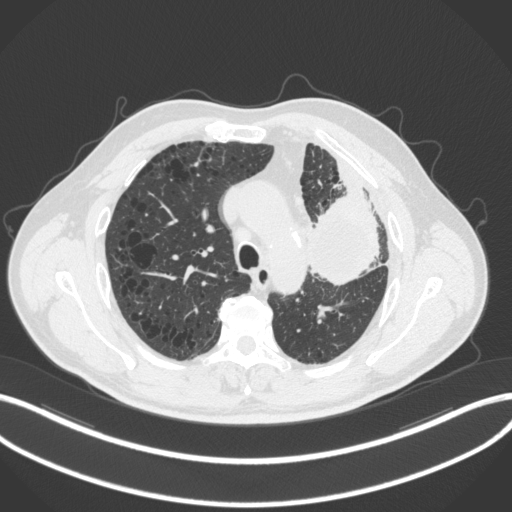
Chest CT, one axial slice; position 211 of 286 along the scan axis; lung window (W 1500 / L -600 HU); 512 × 512 image matrix, field of view 400 × 400 mm. Patient: male, 68 years. Case-level facts recorded for this patient, not image findings: clinical TNM (as recorded): T3 N3 M1.
Outlined on this slice (rectangle marked by the reading radiologist):
- lung tumour (recorded histology: adenocarcinoma): bounding box <306,188,383,289> (left, top, right, bottom; pixels)